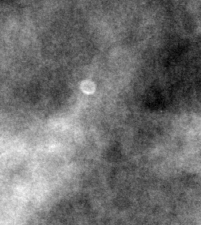
Crop from a digitized film mammogram around one marked abnormality, right breast, MLO view.
Marked abnormality: calcifications, morphology lucent center; BI-RADS assessment category 2; subtlety rating 4 on a 1 (subtle) to 5 (obvious) scale; benign without callback (not worked up further).